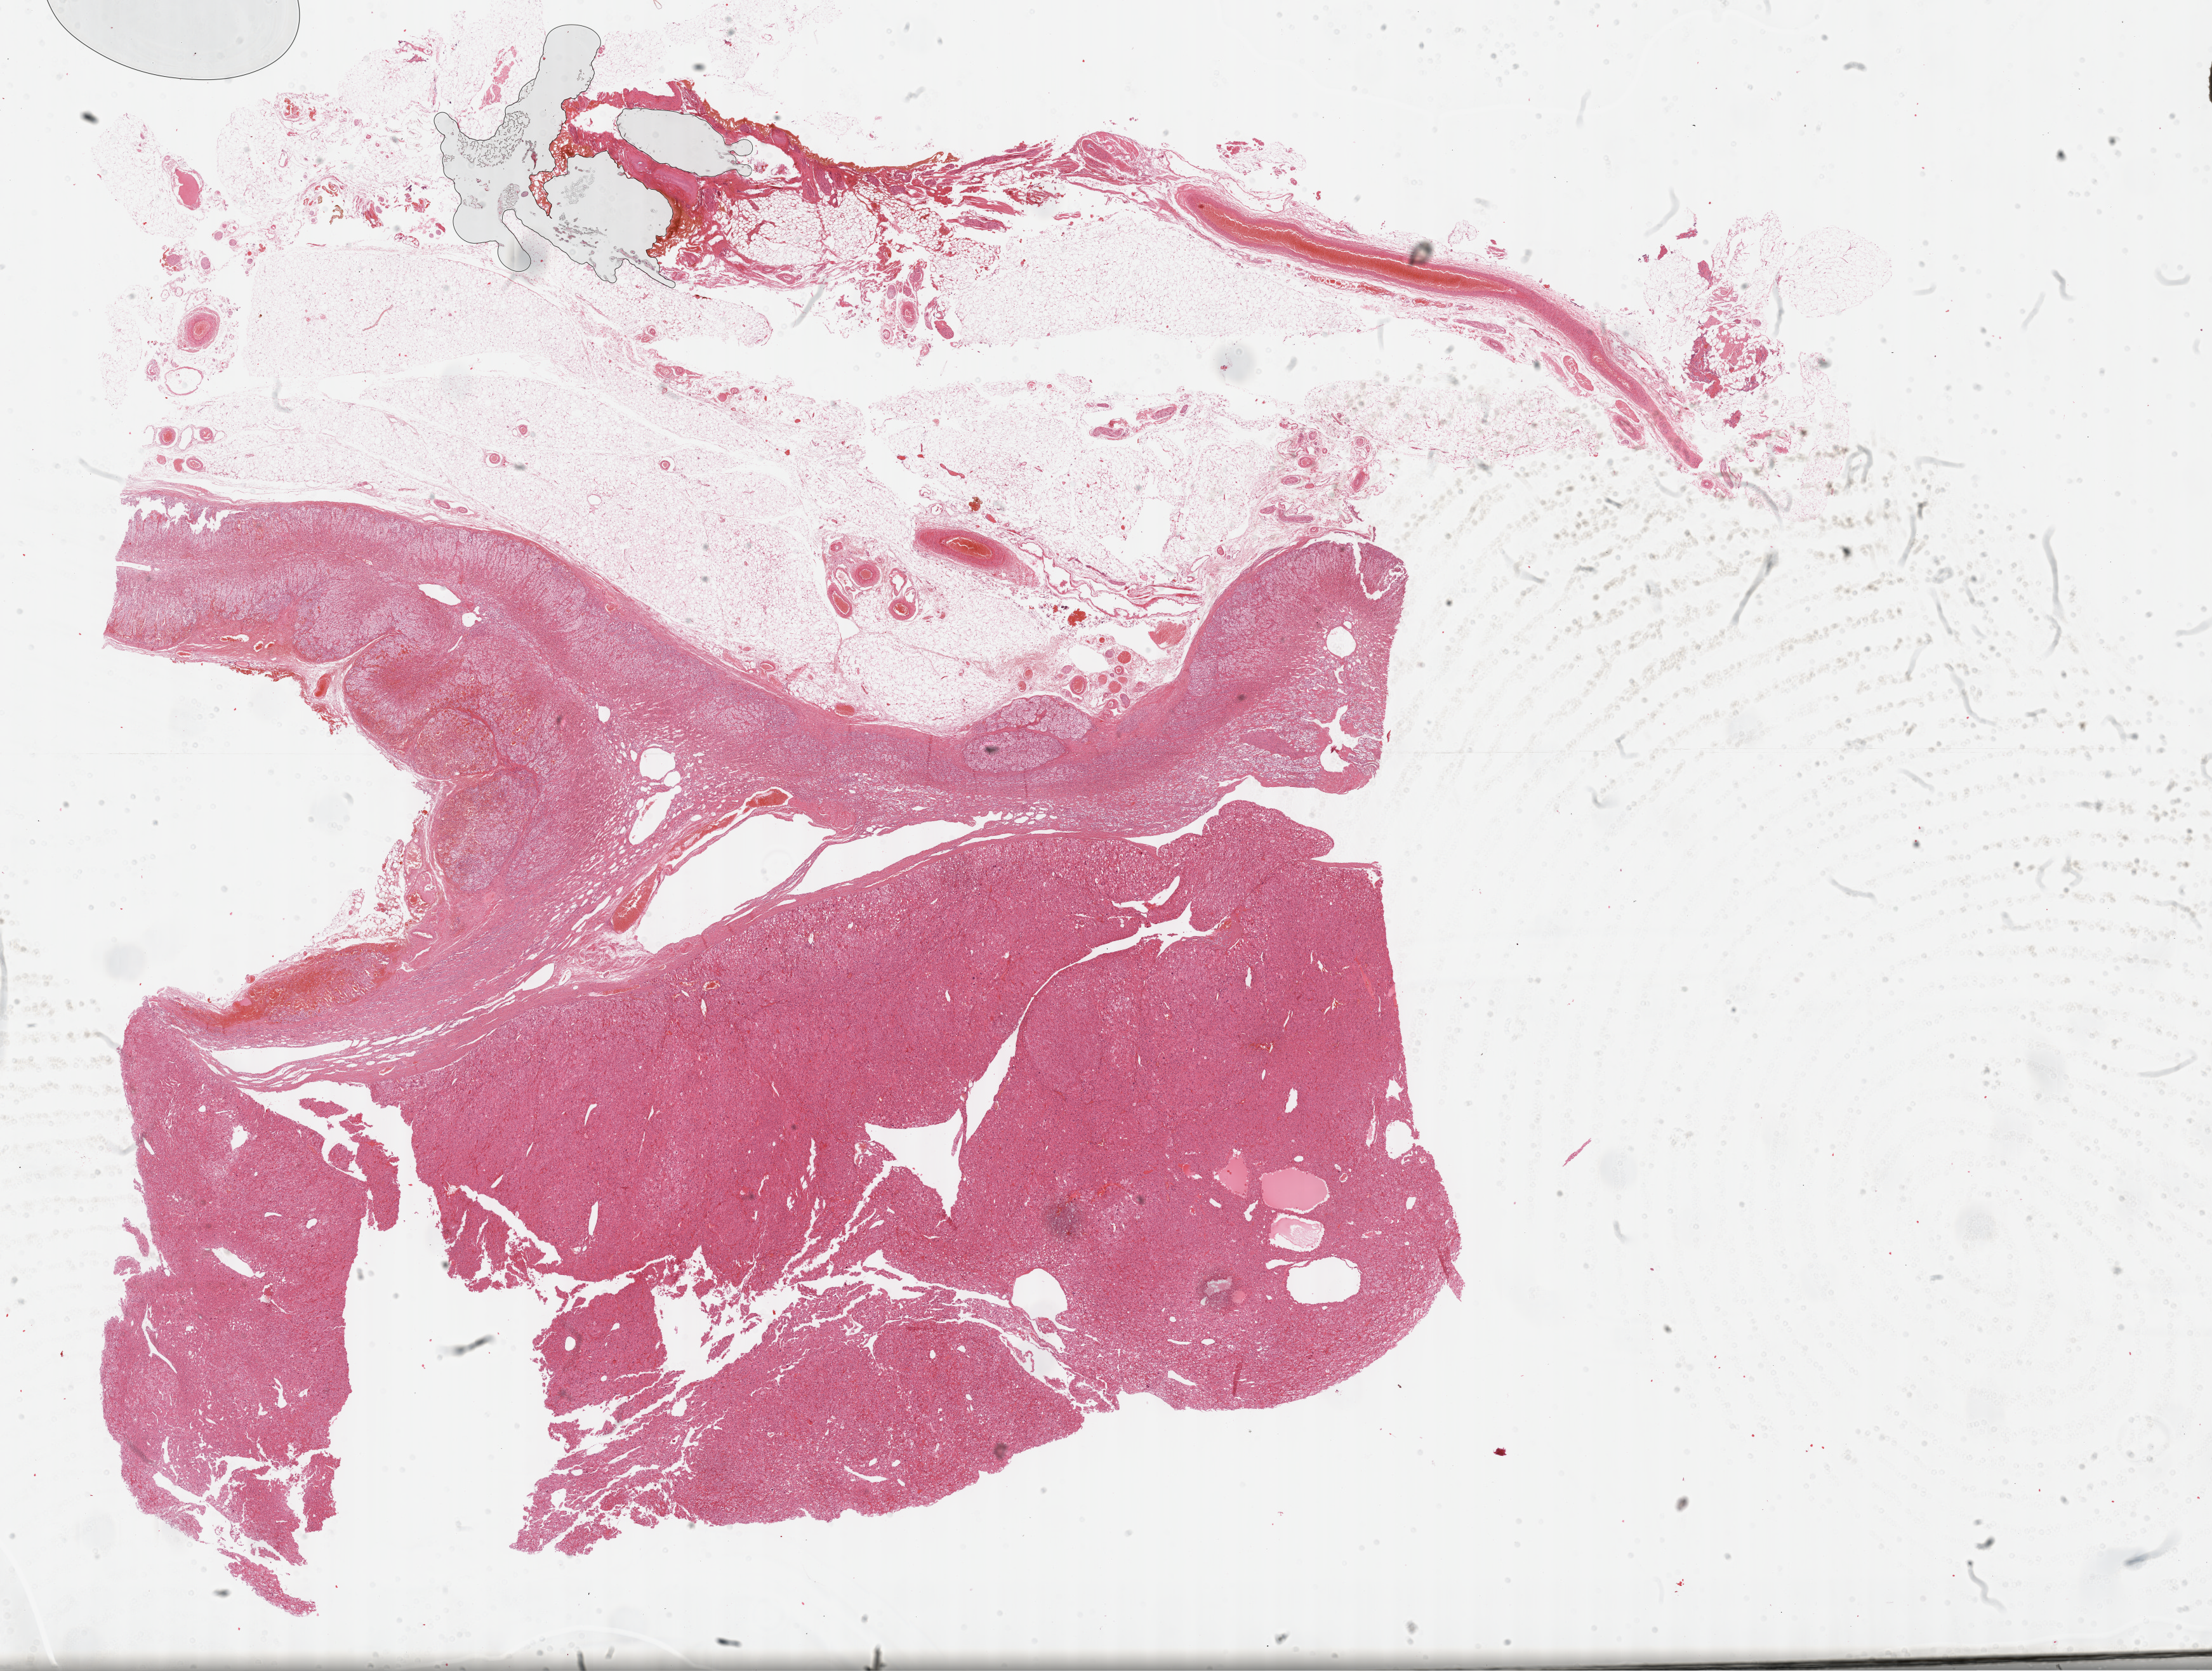
Digitized H&E-stained tissue section (whole slide), whole scanned area (about 28.2 x 21.3 mm, from a 40x scan) shown as a low-resolution overview; formalin-fixed paraffin-embedded (FFPE) diagnostic section; sample: primary tumour, adrenal cortex. Patient: female, age at initial diagnosis 36 years.
* pathologic diagnosis: Adrenal cortical carcinoma (cortex of adrenal gland)